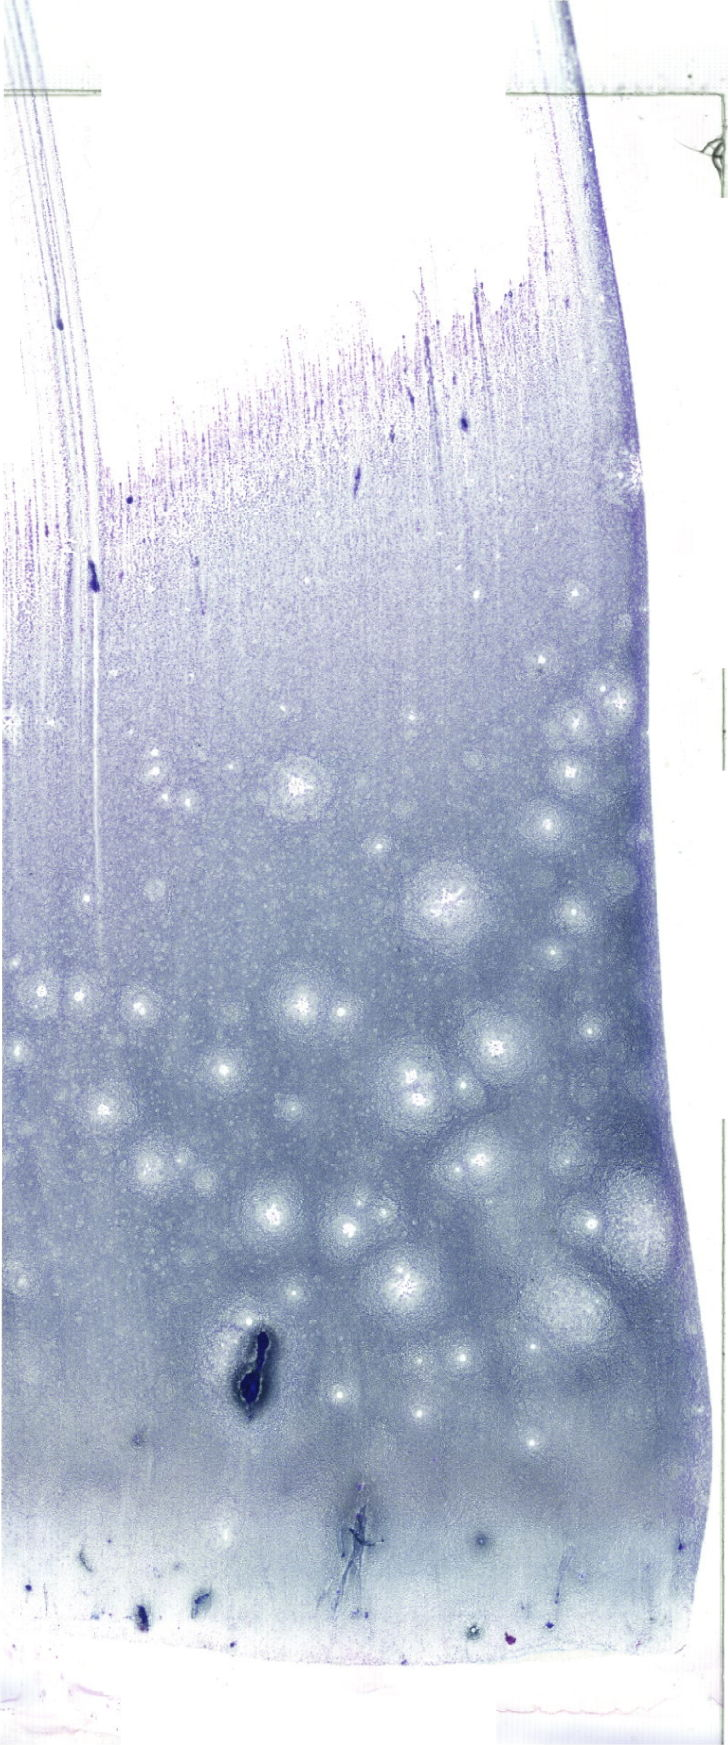
Whole-slide image of a May-Grünwald-Giemsa (MGG)-stained bone marrow aspirate smear — whole scanned area (about 20.6 x 49.5 mm) shown as a low-resolution overview. Patient sex: male.
Diagnosis: Acute Myelomonocytic Leukemia.